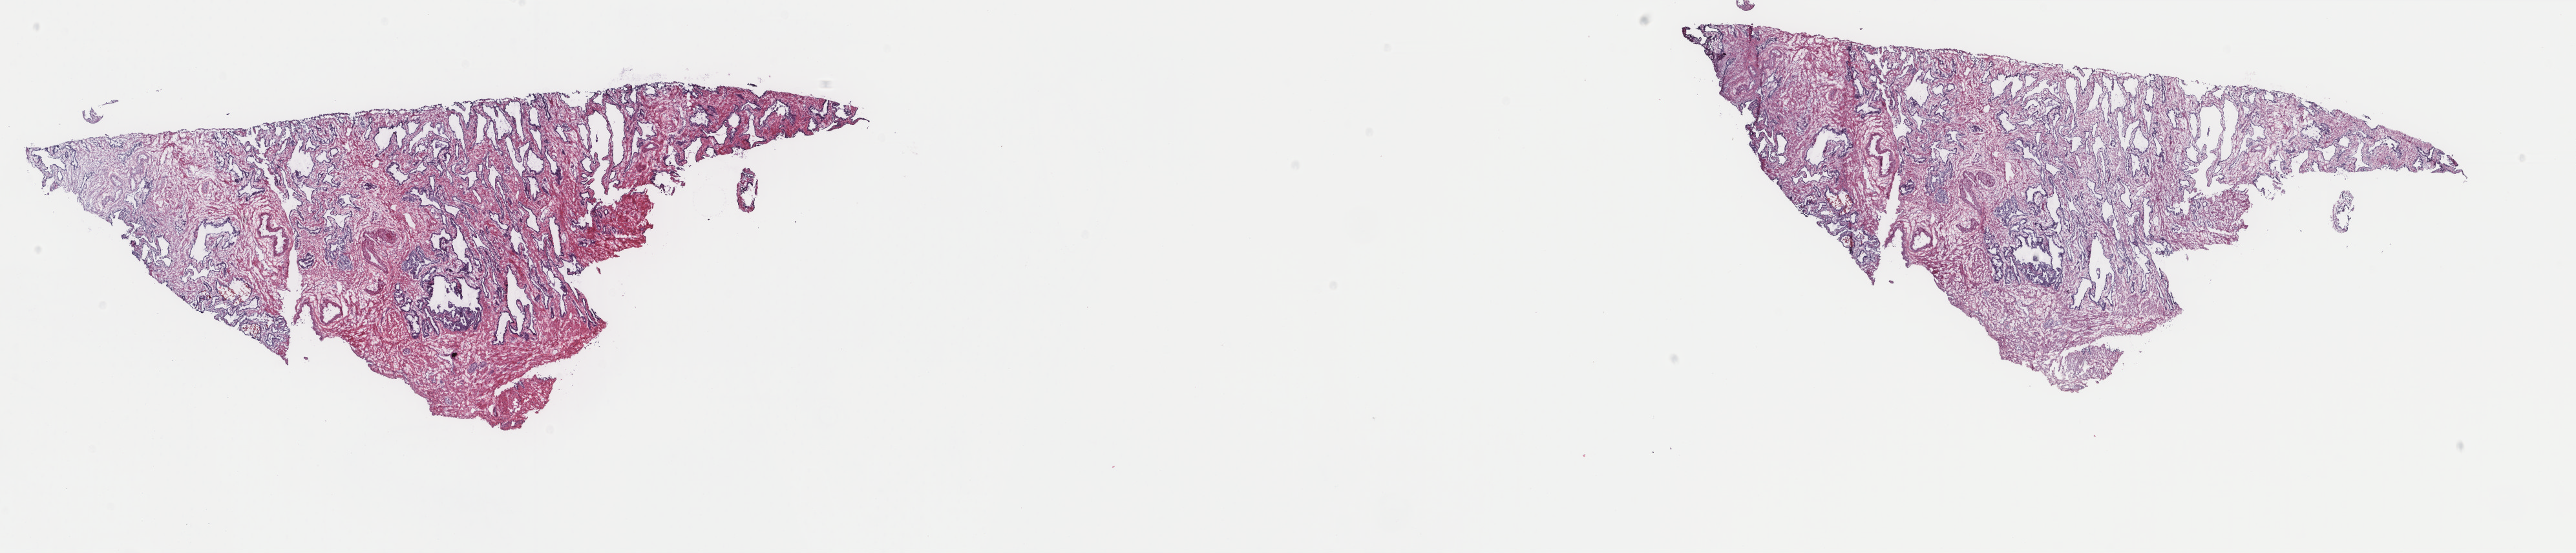
Whole-slide histology image, Hematoxylin and eosin (H&E) stained, shown as a low-resolution overview of the whole scanned area (about 31.6 x 6.8 mm); frozen section from the top of the tissue portion; prostate, primary tumour sample. Male patient; age at initial diagnosis 57 years. Gleason score: 8 (4+4). Slide review estimates, as recorded: tumour cells 50%, tumour nuclei 100%, normal cells 0%, stromal cells 50%, necrosis 0%. Infiltration values recorded for this section: lymphocyte infiltration 1%, monocyte infiltration 0%, neutrophil infiltration 0%.
- diagnosis: Adenocarcinoma, NOS
- lymph nodes positive (case pathology): 0 of 9 examined